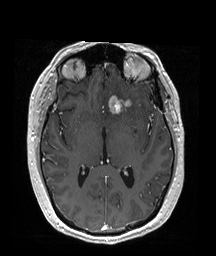
Brain MRI from a brain-tumour surgery series, one axial slice. Position 99 of 192 along the scan axis. T1-weighted post-contrast. 216 × 256 image matrix, field of view 211 × 250 mm. Case-level facts recorded for this patient, not image findings: histopathology: Oligodendroglioma; WHO grade: 2; IDH mutation: yes.
Annotated regions visible in this slice (outlined manually by an expert reader):
- tumour: bounding box (x1, y1, x2, y2) in pixels: (107, 95, 132, 117)